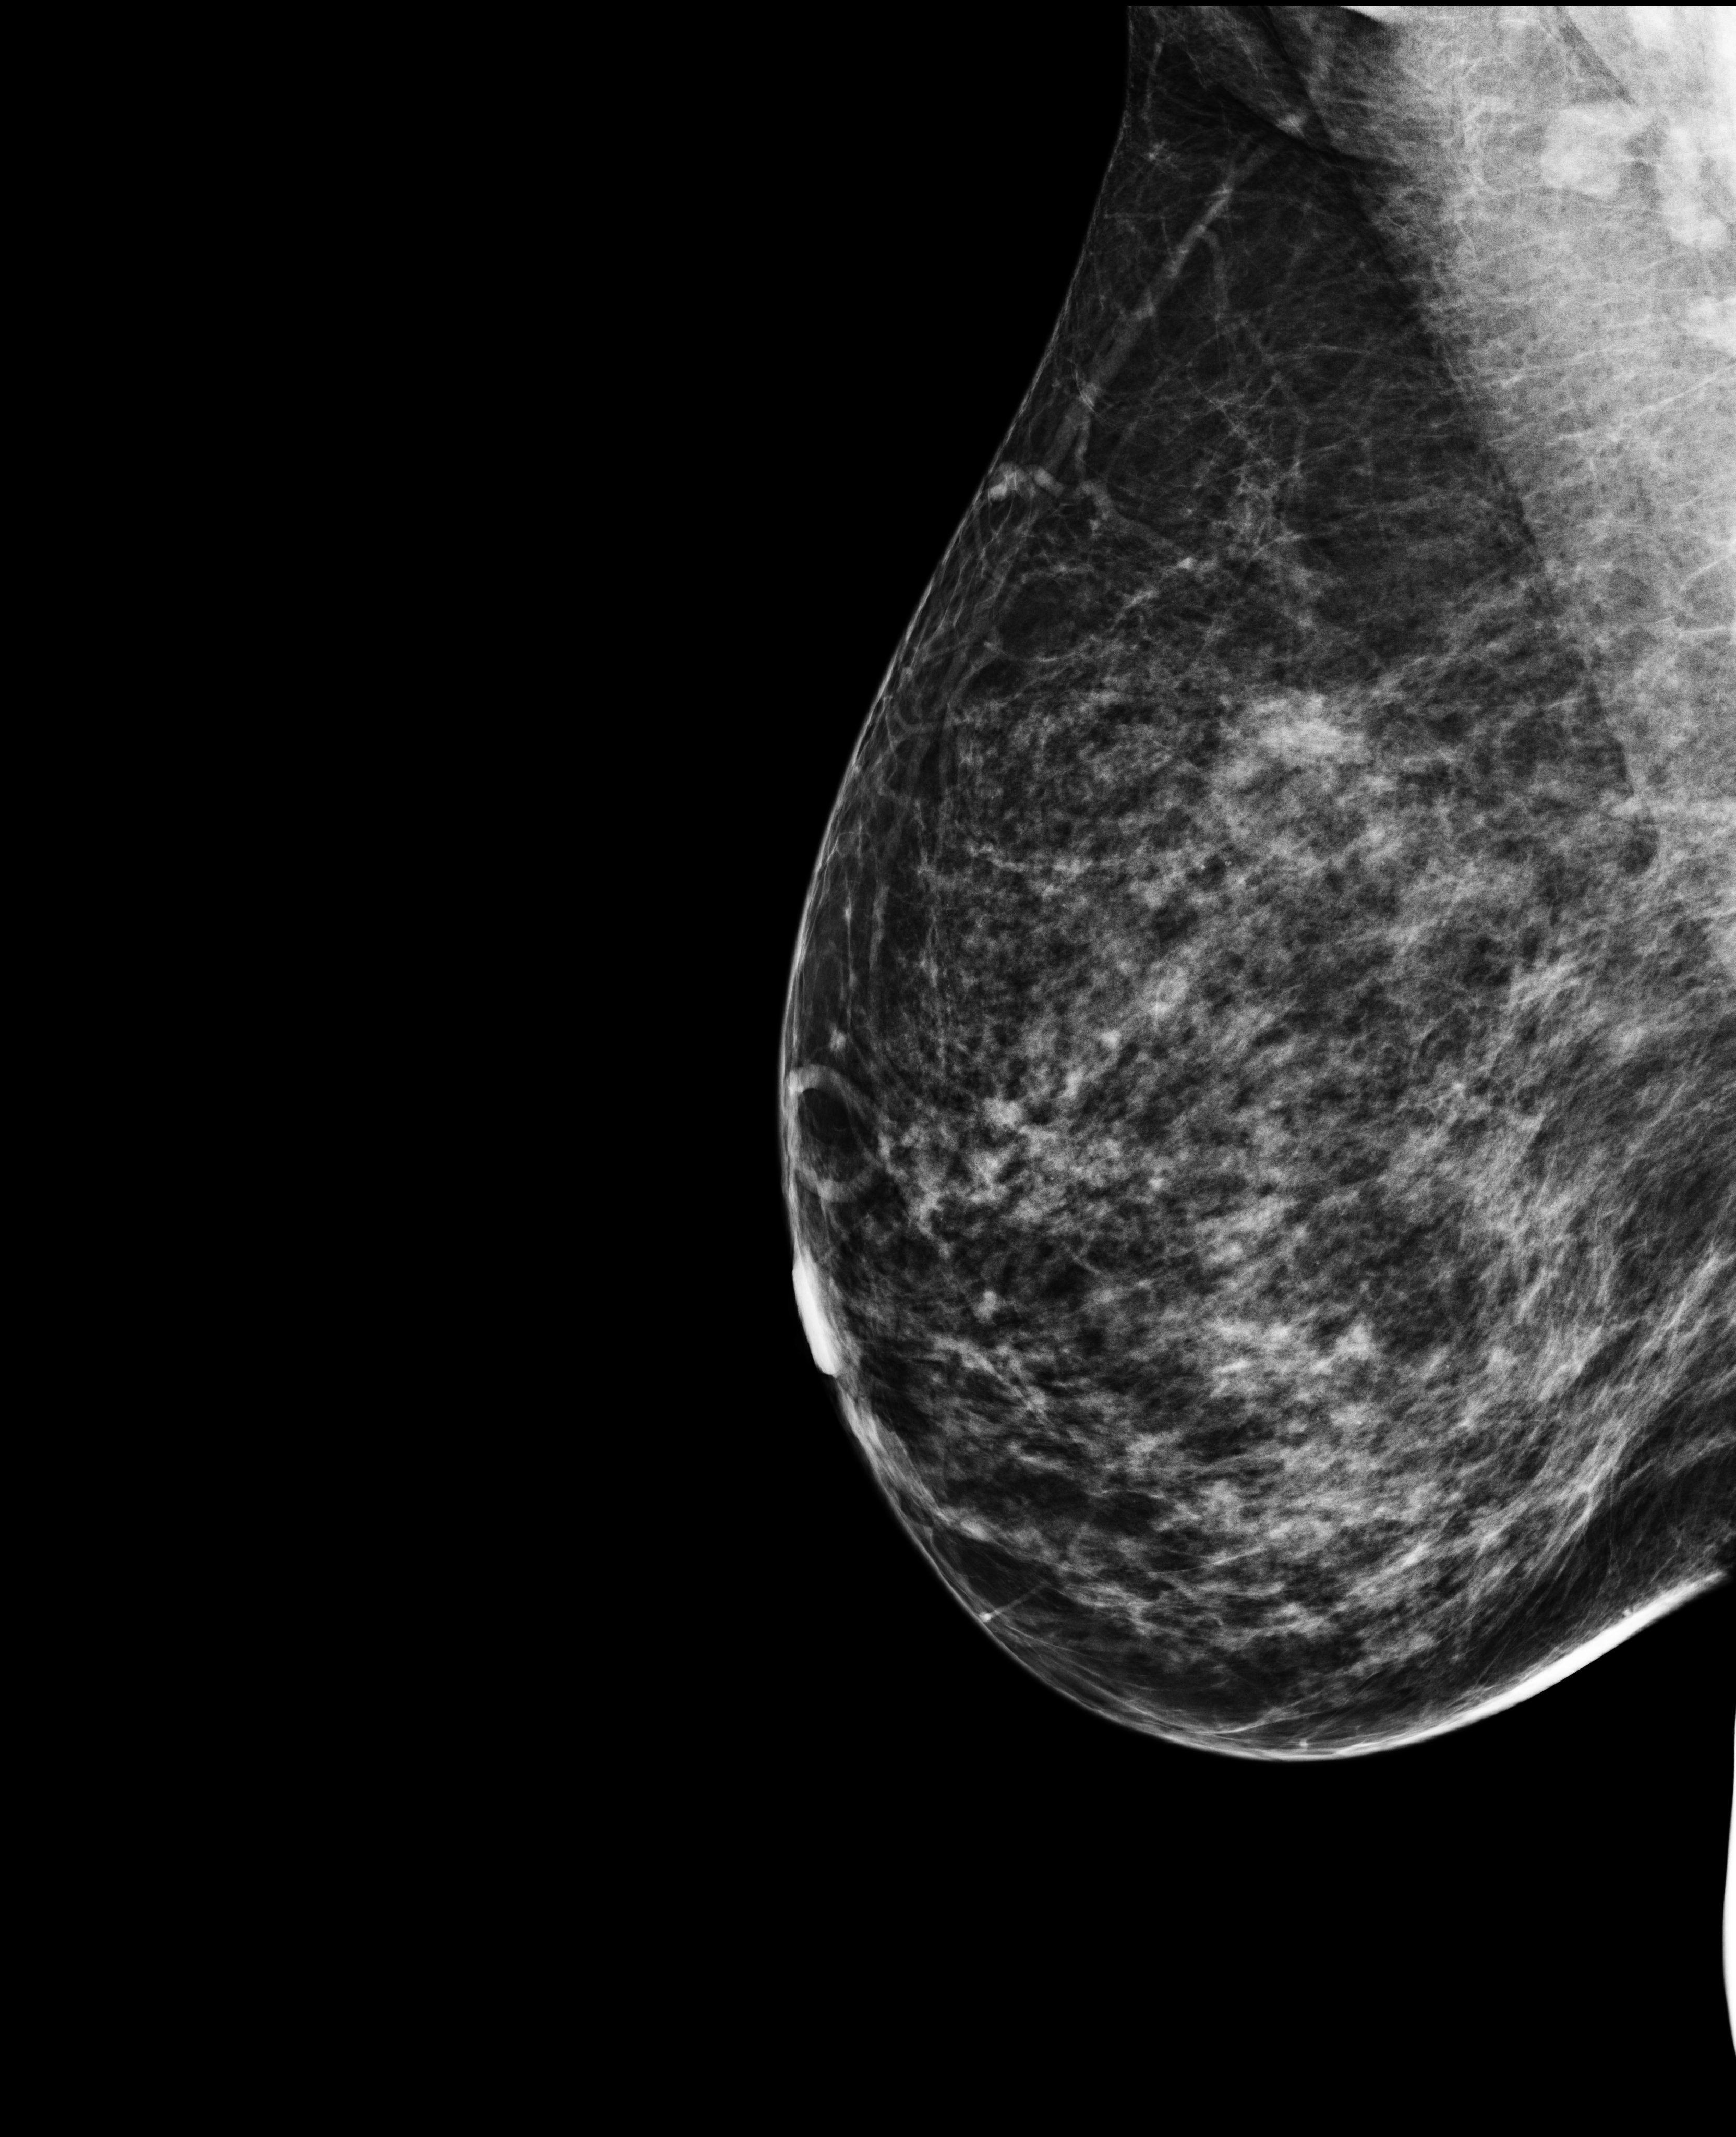
Digital mammogram (FFDM), right breast, MLO view, annual screening mammography examination. Patient aged 50 years (female).
Final BI-RADS category for the screening round (tomosynthesis exam, both breasts): category 1.